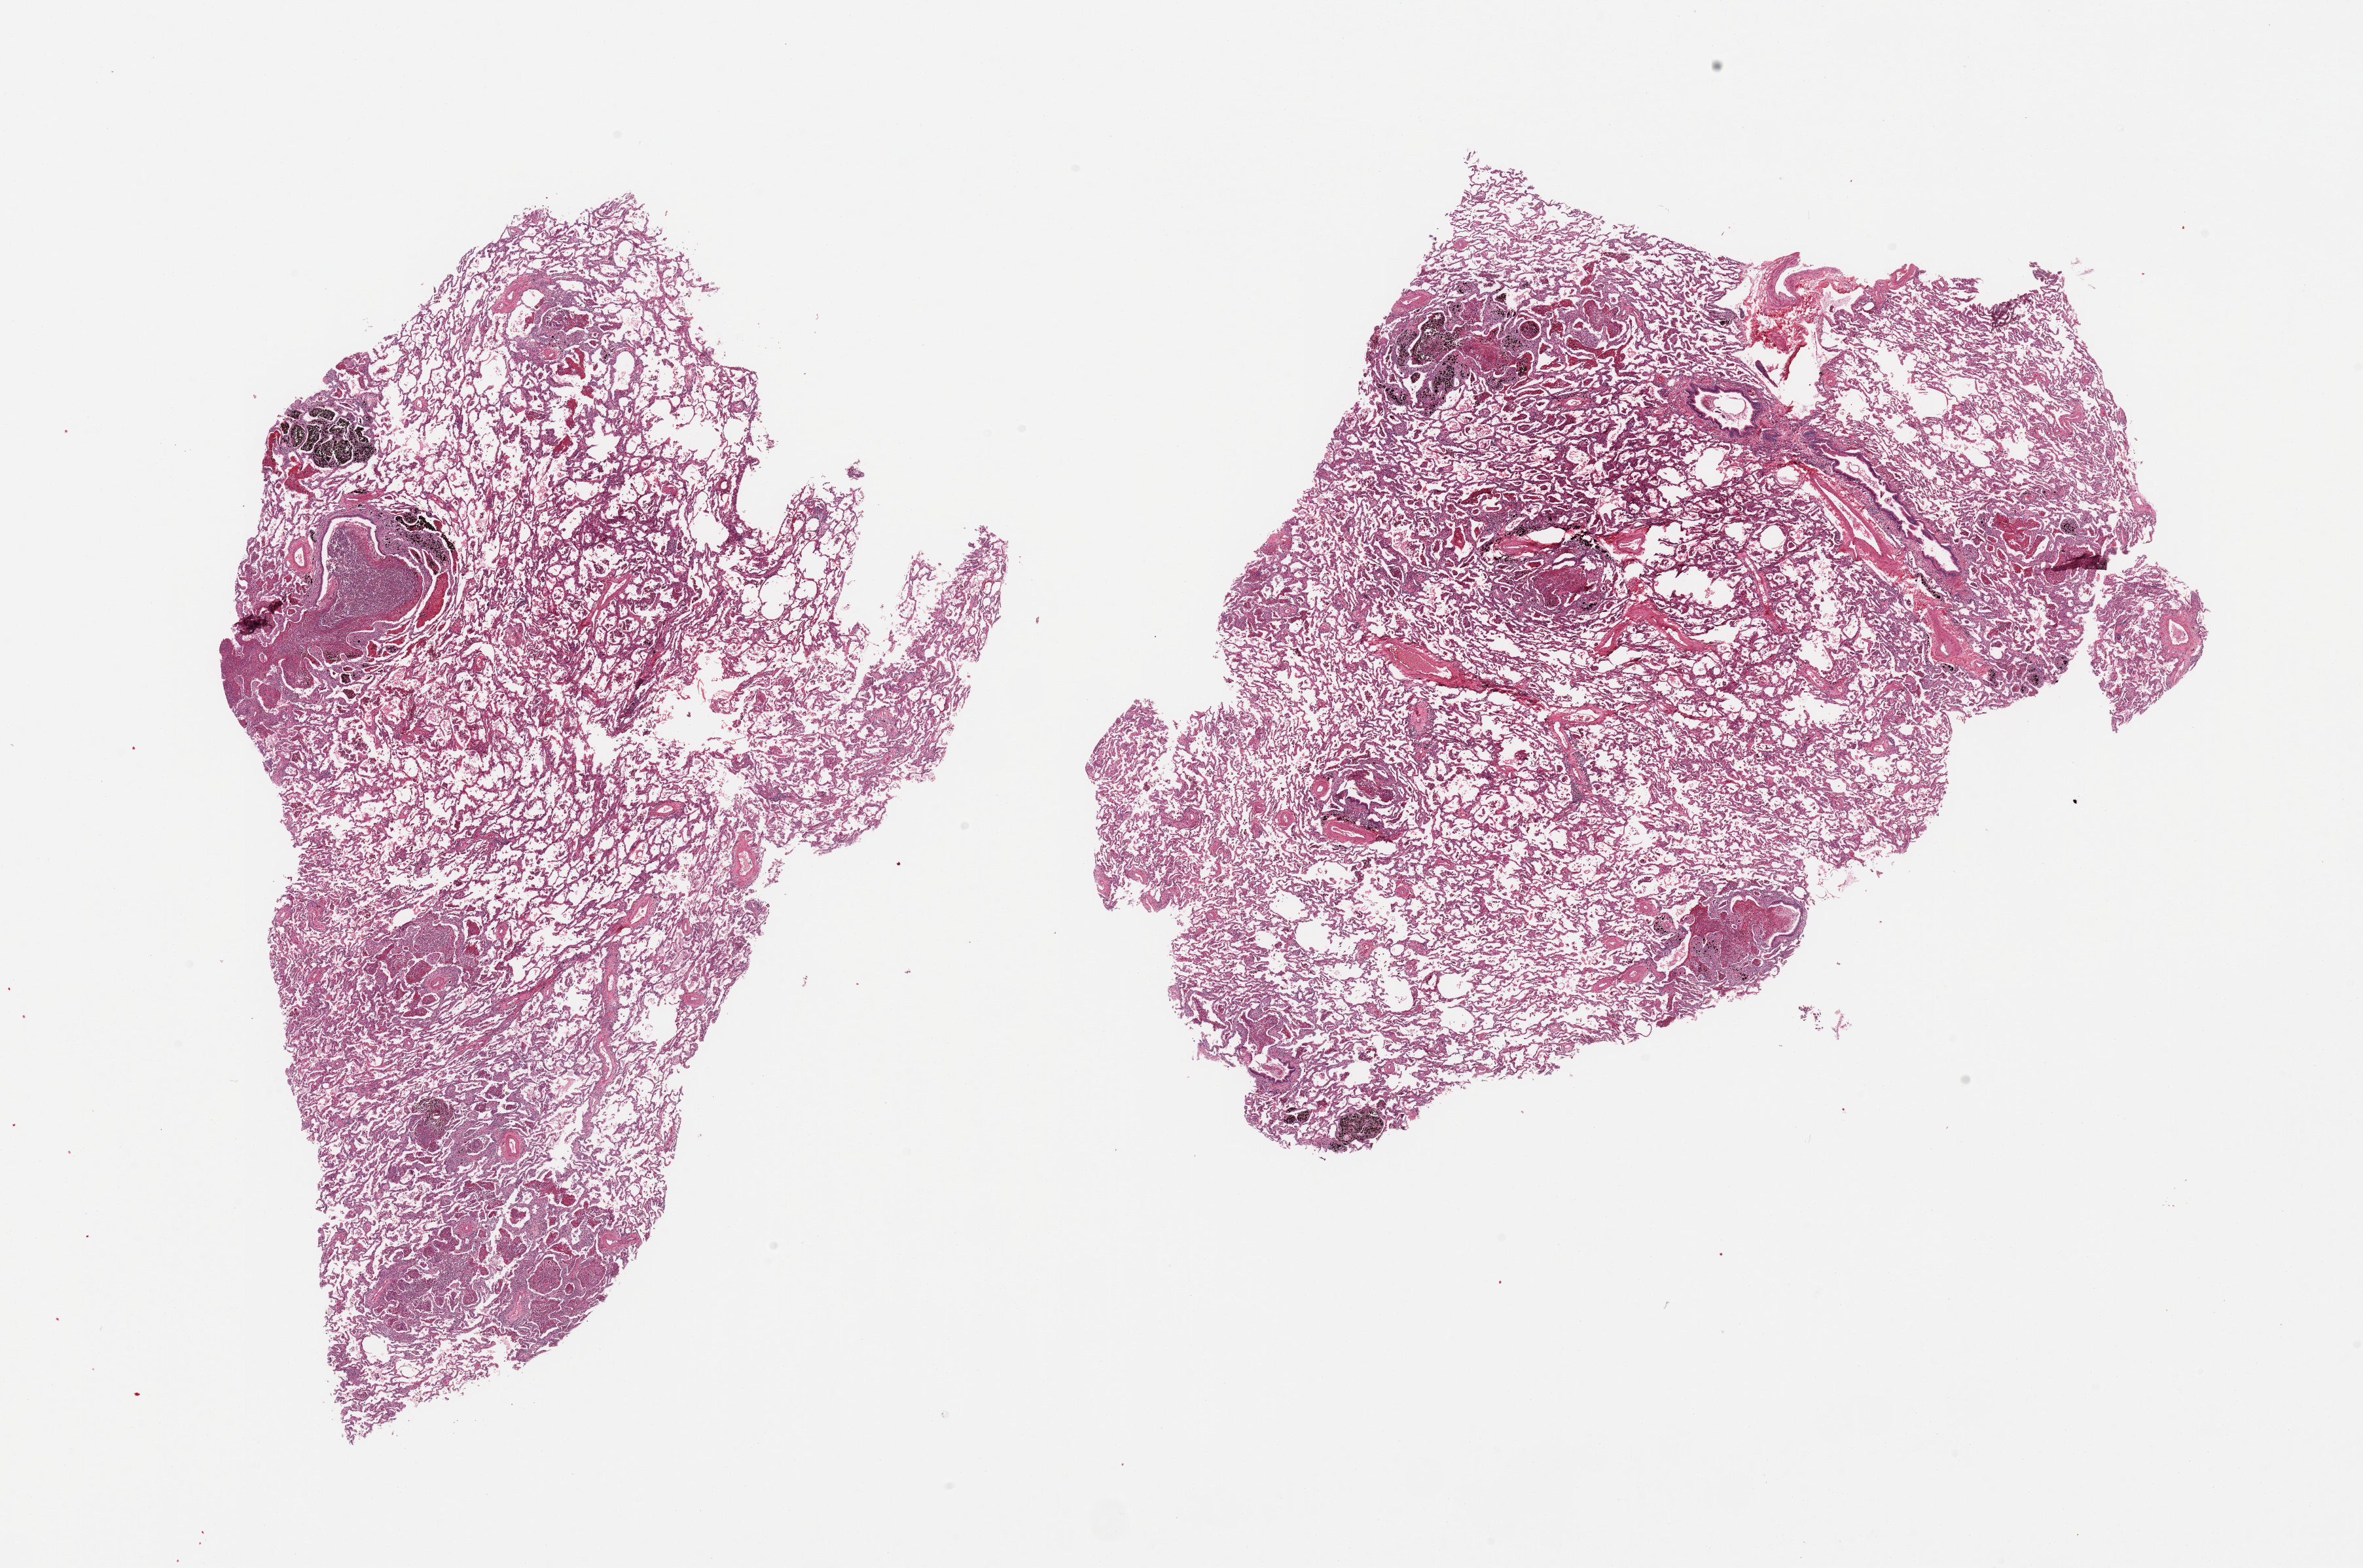
Haematoxylin and eosin whole-slide image, low-resolution overview of the scanned area, about 28.5 x 18.9 mm. PAXgene-fixed paraffin-embedded (PFPE) section. Sampled site (target tissue): lung. Donor tissue sample. Donor: male.
* review note (as recorded): 2 pieces diffuse interstitial mixed inflammation and acute/purulent bronchoitis/bronchioliits. Reviewed by NIH consult panel